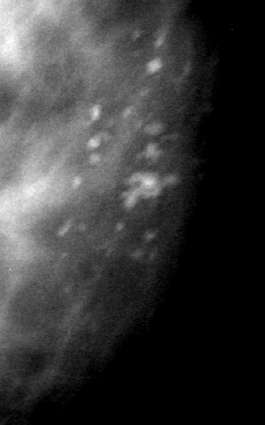
Region of interest cut from a scanned film mammogram (one marked finding); left breast; CC view.
Calcifications, morphology pleomorphic, distribution clustered; BI-RADS assessment category 4; subtlety rating 4 on a 1 (subtle) to 5 (obvious) scale; pathology result (as recorded, not read from the image): malignant.